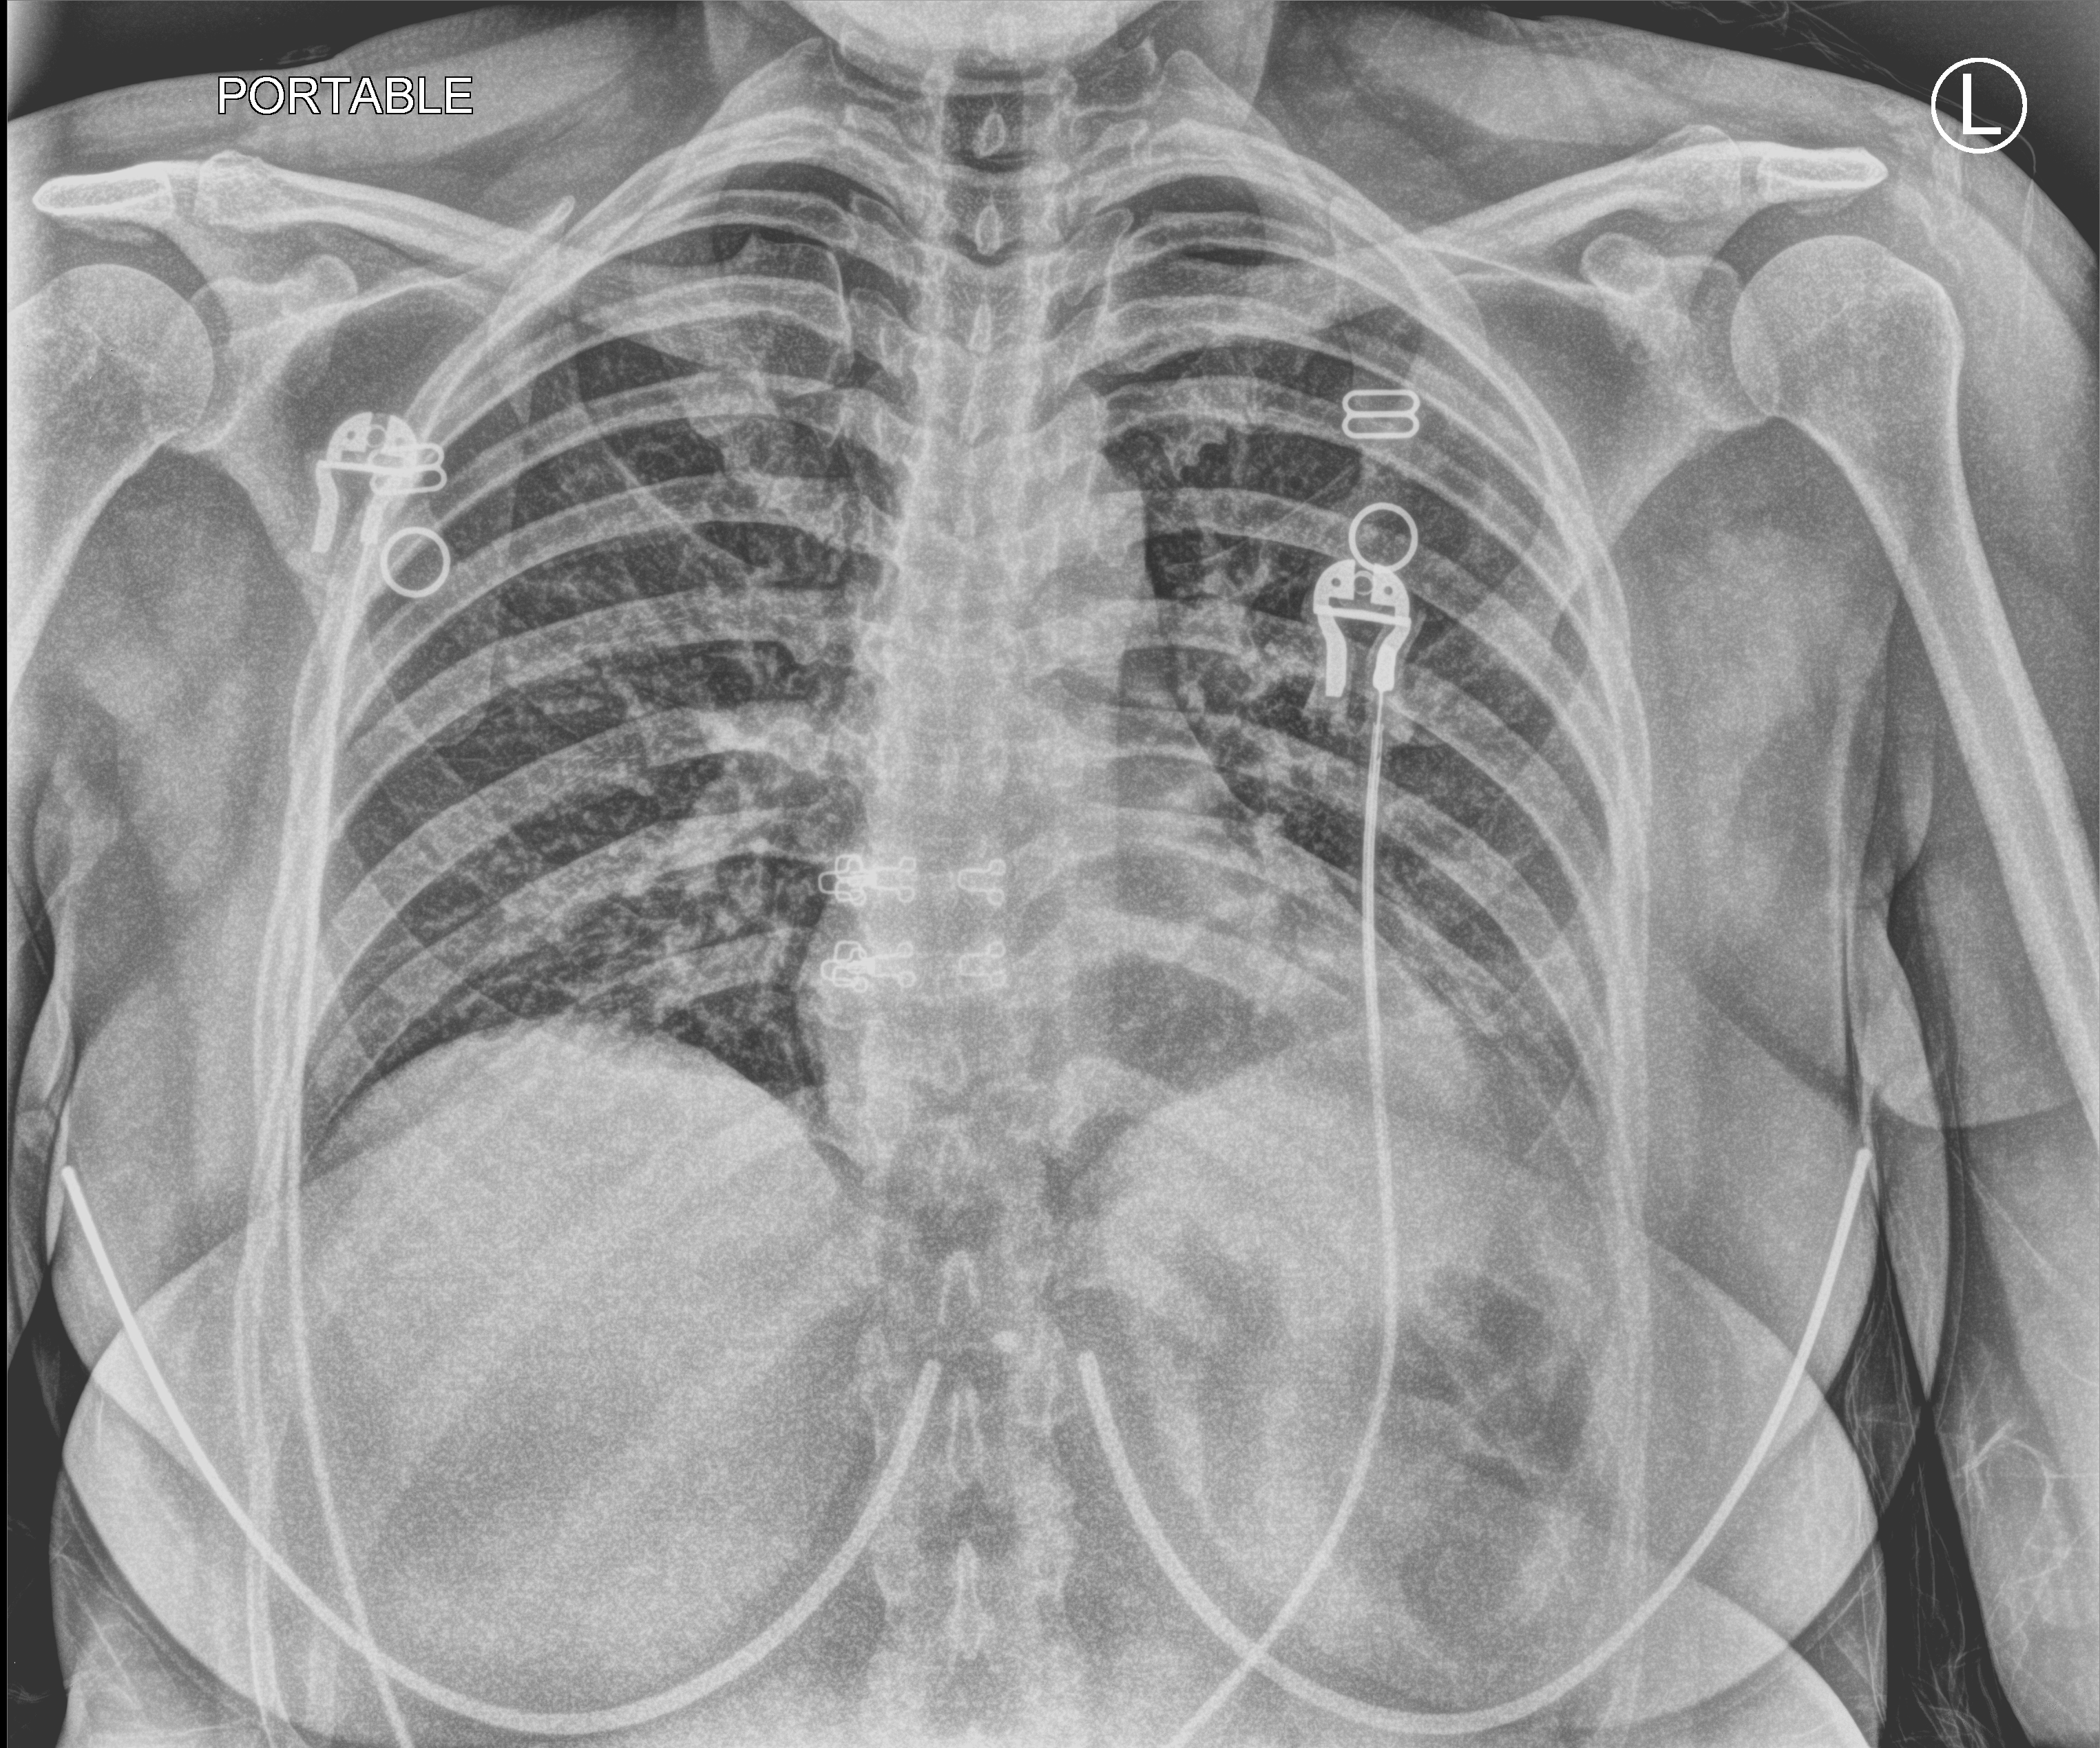
Bedside chest radiograph (computed radiography); anteroposterior (AP) projection. Patient hospitalised with COVID-19; female, aged 18–59 years.
Admission-level facts for this patient (not findings on this image; timing relative to this image not recorded):
- mechanically ventilated during this hospital stay: no
- admitted to intensive care during this hospital stay: no